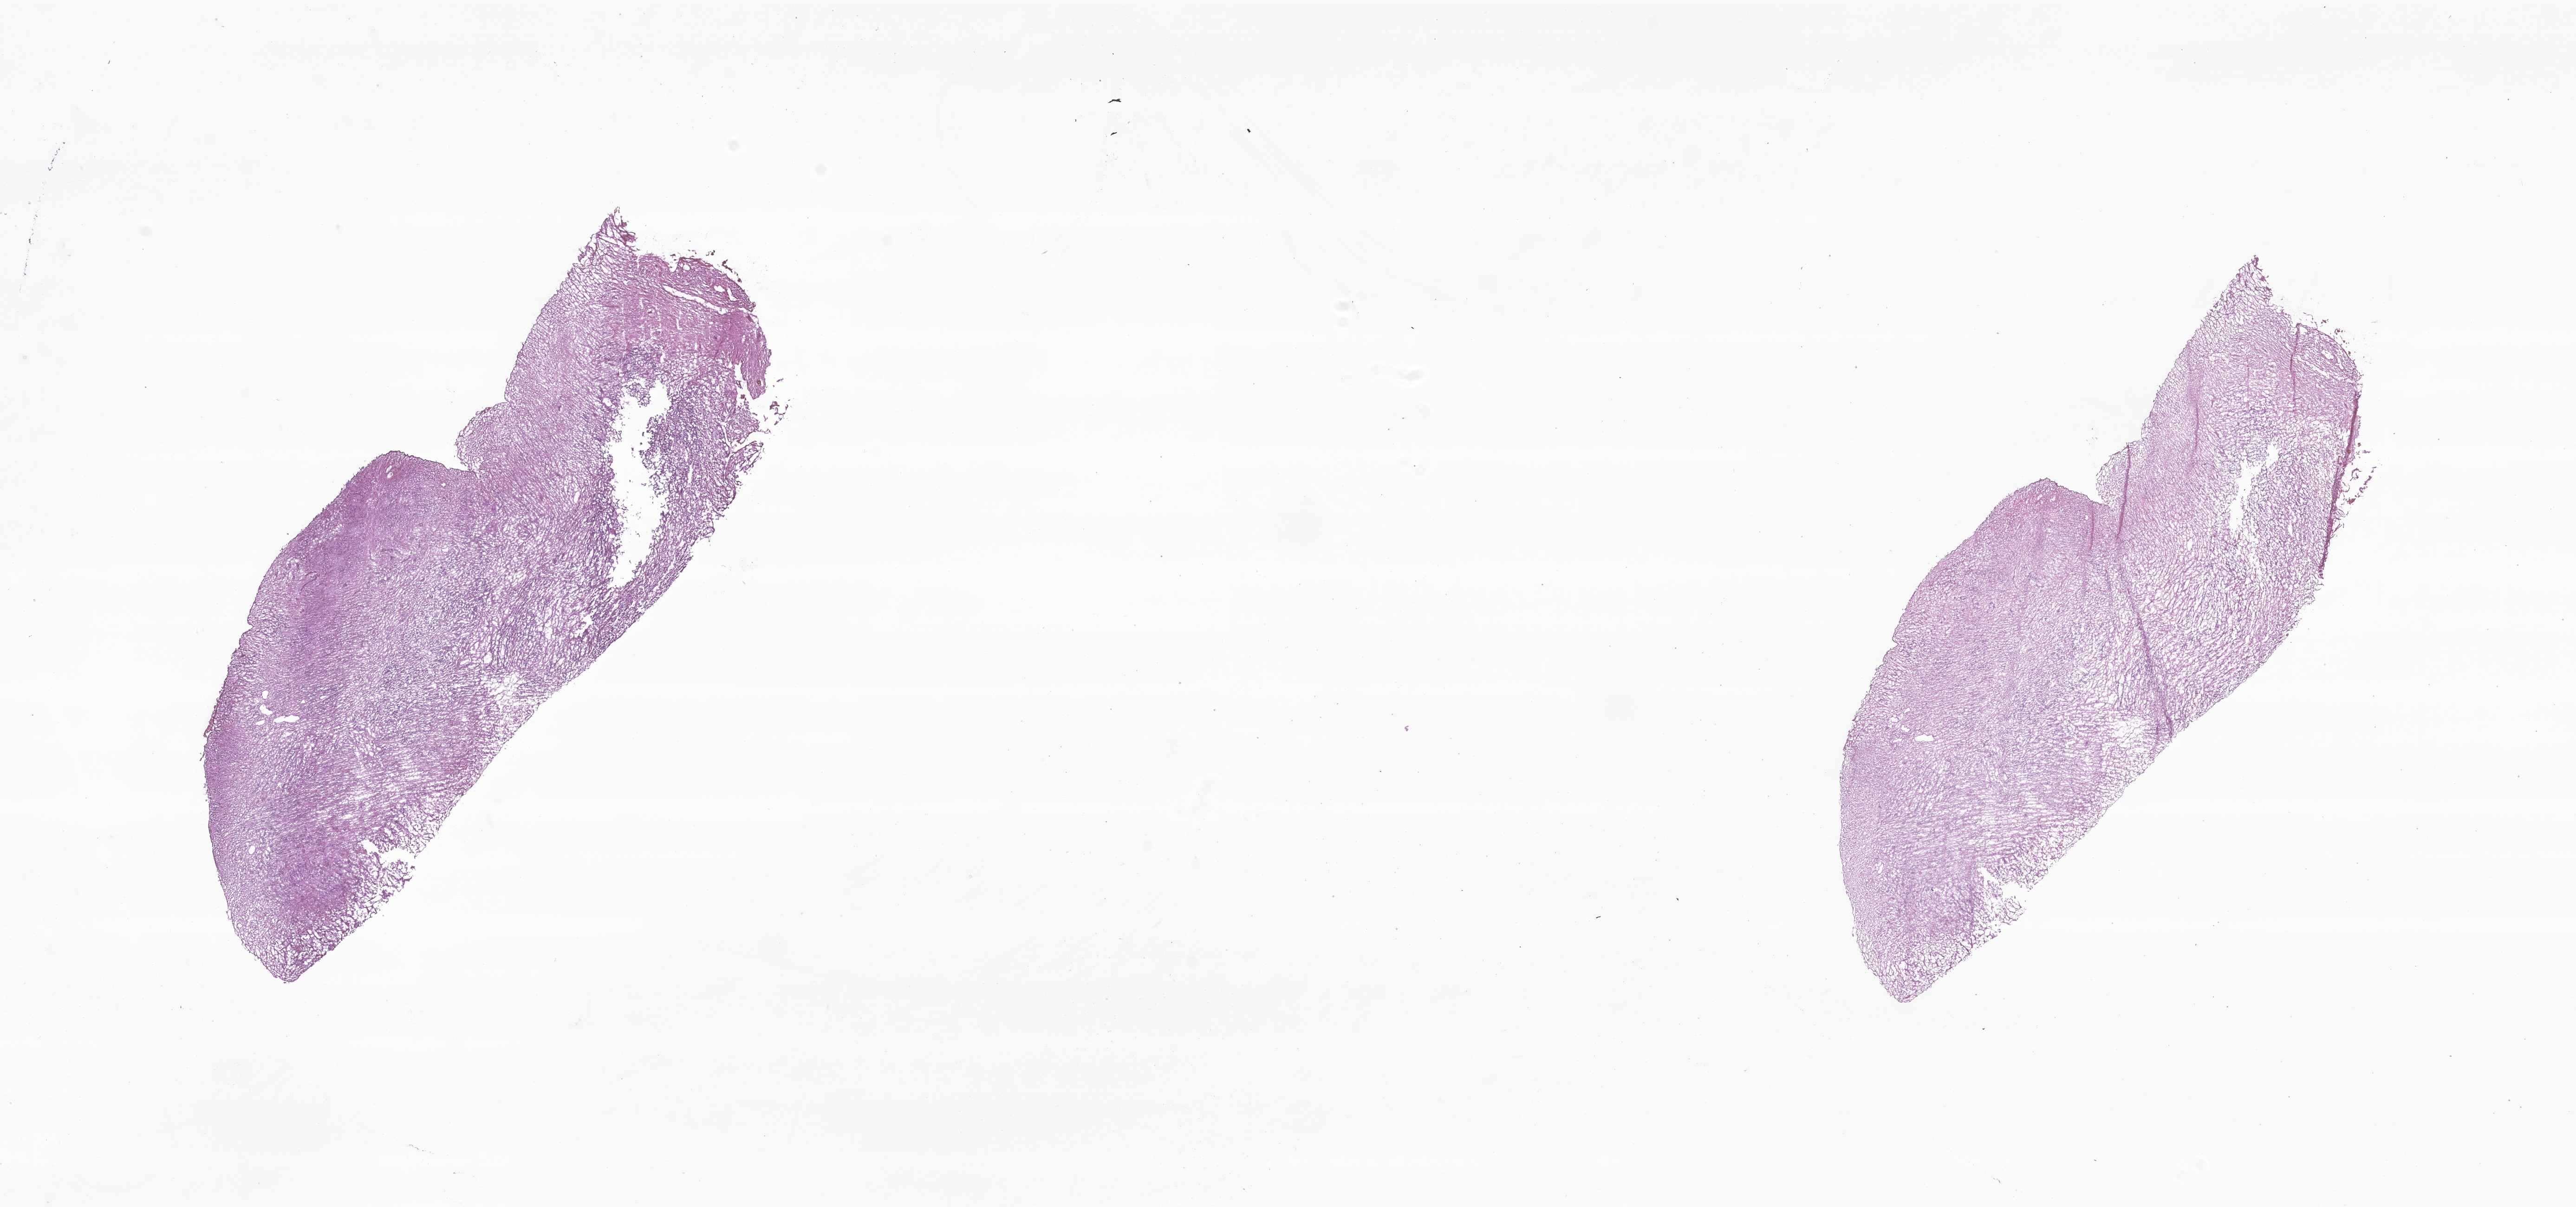
Whole-slide image, H&E stain of tumor tissue from the brain stem — low-resolution overview of the scanned area, about 23.4 x 11.0 mm. Frozen section. Male patient, age 539 days (about 1.5 years).
Diagnosis: Ependymoma, anaplastic.